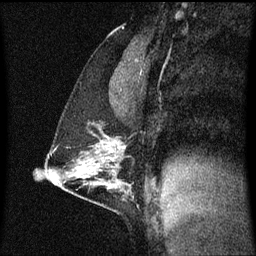
Breast MRI (dynamic contrast-enhanced), one sagittal slice. Position 35 of 60 along the scan axis. Dynamic contrast-enhanced series, image 2 of 3 at this slice position (ordered by acquisition). 1.5 T. TE 4.2 ms, TR 8.4 ms. 256 × 256 image matrix, field of view 200 × 200 mm. Female patient, age 40 years. From the clinical record (not read from this slice): setting: breast cancer imaged before/during neoadjuvant chemotherapy; receptor status: triple-negative.
Structures marked on this image (semi-automatically segmented with operator editing):
- analysis volume of interest (the breast-tissue region the enhancement analysis was run in; not a lesion): box from (x=43, y=124) to (x=132, y=195) px
- tumour enhancement mask (voxels above the 70 % enhancement threshold inside the analysis volume of interest): (x=111, y=144)–(x=126, y=153)